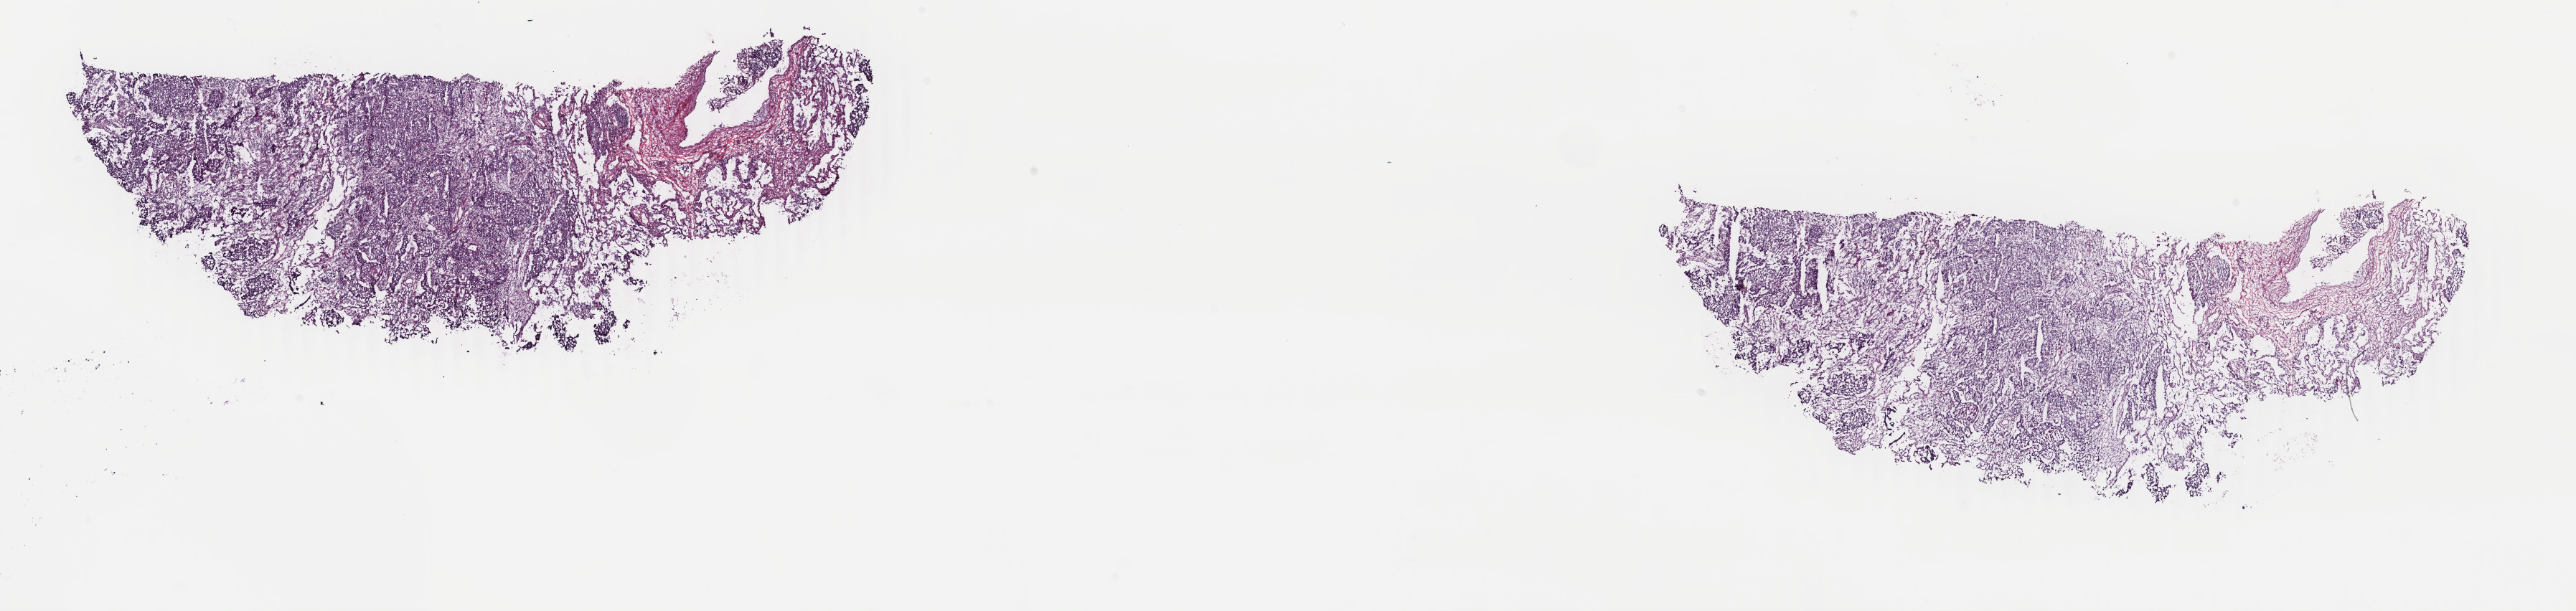
Digitized H&E-stained tissue section (whole slide), low-resolution overview of the scanned area, about 28.6 x 6.8 mm (acquisition: 40x scan). Frozen section. Sample: primary tumour, lung. Female, age 66 years at initial diagnosis. Pathologist review of this section (percent, as recorded): tumour cells 100%, tumour nuclei 70%, normal cells 0%, stromal cells 0%, necrosis 0%. Inflammatory infiltration, as recorded: lymphocyte infiltration 5%, monocyte infiltration 4%, neutrophil infiltration 2%.
• histologic diagnosis: Acinar cell carcinoma
• AJCC pathologic stage: IIIA (7th edition)
• TNM: T2b N2 M0